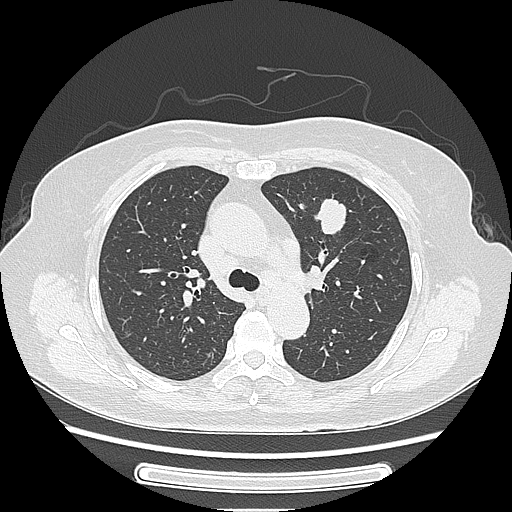
Chest CT, one axial slice. Slice 164 of 227 in the series (ordered by position). Reconstruction kernel LUNG. 120 kVp. Lung window (W 1500 / L -600 HU). 1.25 mm slice thickness. 512 × 512 image matrix. Female patient, age 77 years. From the clinical record (not read from this slice): clinical TNM (as recorded): T1c N3 M0; histopathological grade: G2-3.
Outlined on this slice (bounding box drawn by a radiologist):
- lung tumour (recorded histology: adenocarcinoma): bounding box <314,195,365,251> (left, top, right, bottom; pixels)